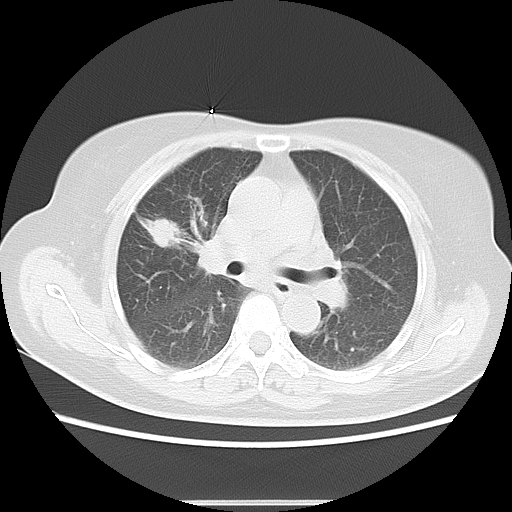
Chest CT, one axial slice; reconstruction kernel LUNG; 120 kVp; lung window (W 1500 / L -600 HU); 512 × 512 image matrix. Female patient, age 57 years. Case-level facts recorded for this patient, not image findings: clinical TNM (as recorded): T1c N1 M0.
Structures marked on this image (bounding box drawn by a radiologist):
- lung tumour (recorded histology: adenocarcinoma): bounding box [x1, y1, x2, y2] px = [142, 206, 184, 256]